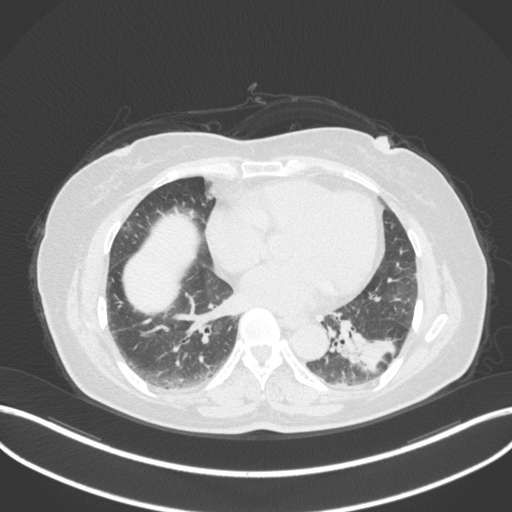
Chest CT, one axial slice; position 151 of 307 along the scan axis; reconstruction kernel B31f; 120 kVp; lung window (W 1500 / L -600 HU); 512 × 512 image matrix, field of view 400 × 400 mm. Patient: female, 59 years. From the clinical record (not read from this slice): clinical TNM (as recorded): T2a N0 M0; histopathological grade: G2-3.
Outlined on this slice (rectangle marked by the reading radiologist):
- lung tumour (recorded histology: adenocarcinoma): bounding box (x1, y1, x2, y2) in pixels: (329, 318, 401, 375)